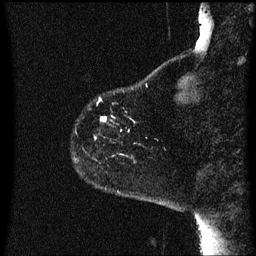
Breast MRI (dynamic contrast-enhanced), one sagittal slice. Dynamic contrast-enhanced series, image 2 of 3 at this slice position (ordered by acquisition). 1.5 T. TE 4.2 ms, TR 8 ms. 2 mm slice thickness. 256 × 256 image matrix, field of view 200 × 200 mm. Female patient, age 60 years.
Structures marked on this image (semi-automatic segmentation, software-assisted and operator-edited):
- analysis volume of interest (the breast-tissue region the enhancement analysis was run in; not a lesion): box from (x=95, y=98) to (x=136, y=161) px
- tumour enhancement mask (voxels above the 70 % enhancement threshold inside the analysis volume of interest): (x=96, y=118)–(x=107, y=139)